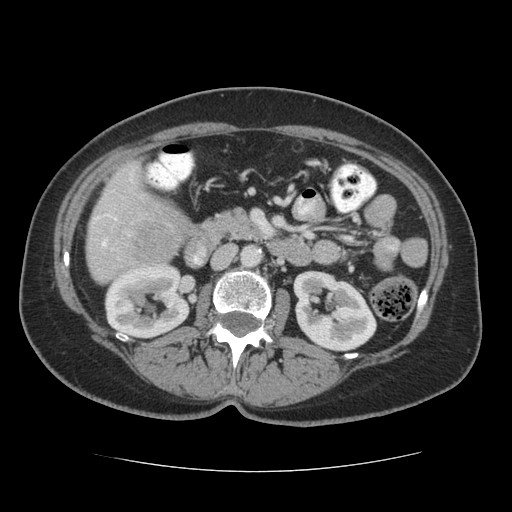
Contrast-enhanced abdominal CT (liver protocol), one axial slice; slice 15 of 75 in the series (ordered by position); reconstruction kernel STANDARD; soft-tissue window (W 400 / L 40 HU); 2.5 mm slice thickness; 512 × 512 image matrix. Case-level facts recorded for this patient, not image findings: diagnosis: hepatocellular carcinoma (patient treated with transarterial chemoembolisation; whether this scan precedes or follows treatment is not stated here); TNM stage (as recorded): Stage-I; Child-Pugh class: A; tumour differentiation: moderately differentiated.
Annotated regions visible in this slice (semi-automatic segmentation, software-assisted and operator-edited):
- liver parenchyma outside the tumour (the mass and vessels are separate outlines, so this box may not span the whole liver): box from (x=86, y=160) to (x=188, y=282) px
- mass: (x=125, y=204)–(x=184, y=265)
- liver vessels: (x=94, y=170)–(x=134, y=250)